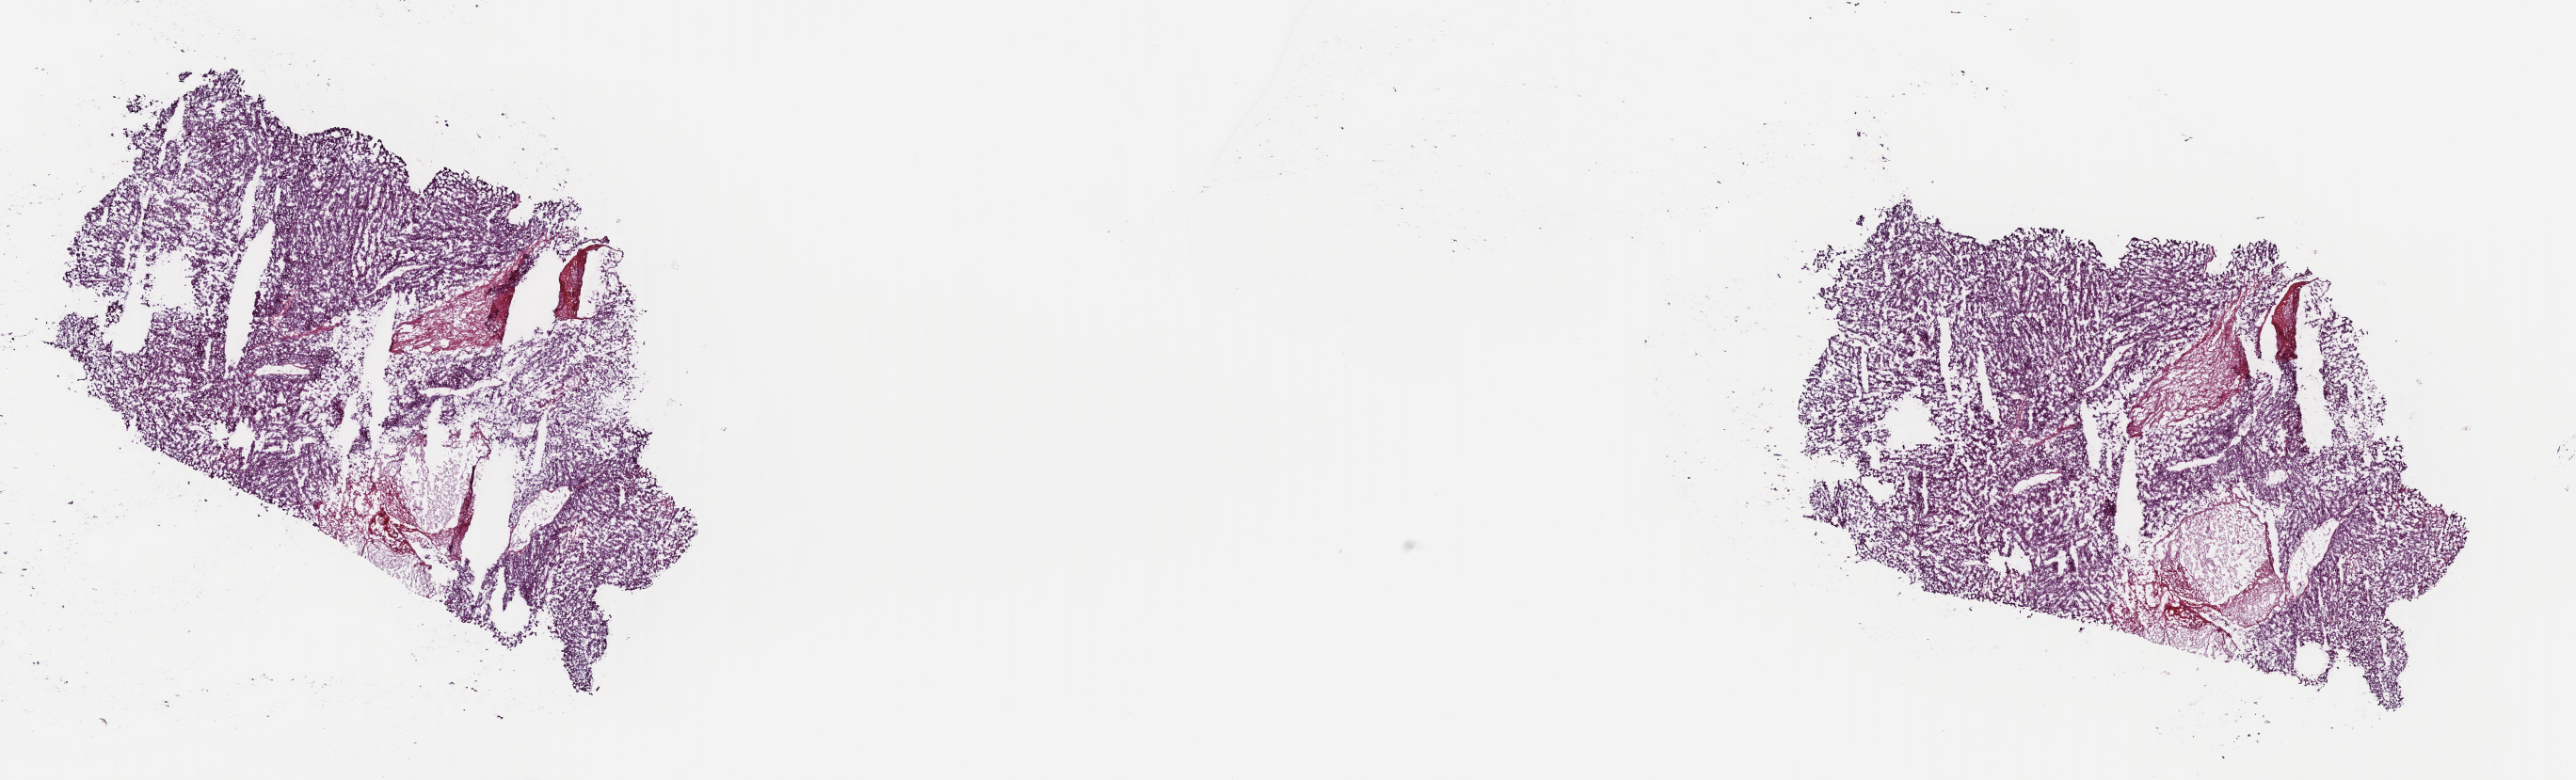
H&E whole-slide image, a low-resolution overview of the entire scanned area, about 21.6 x 6.5 mm (acquisition: 40x scan), frozen section from the top of the tissue portion, adrenal cortex, primary tumour sample. Patient: male, age at initial diagnosis 53 years. Slide review estimates, as recorded: tumour cells 88%, tumour nuclei 100%, normal cells 0%, stromal cells 10%, necrosis 2%. Inflammatory infiltration, as recorded: lymphocyte infiltration 0%, monocyte infiltration 0%, neutrophil infiltration 0%.
* diagnosis: Adrenal cortical carcinoma (cortex of adrenal gland)